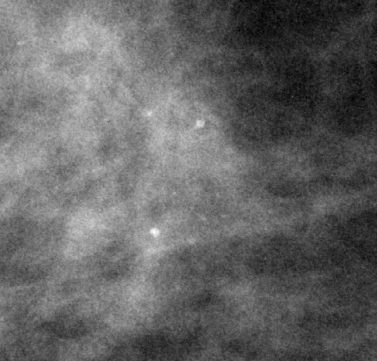
Cropped region of a digitized screen-film mammogram centred on a radiologist-marked abnormality, right breast, CC view, BI-RADS breast density category 2 (scale 1–4).
Calcifications, morphology pleomorphic, distribution clustered; BI-RADS assessment category 3; subtlety rating 3 on a 1 (subtle) to 5 (obvious) scale; pathology (as recorded): benign.